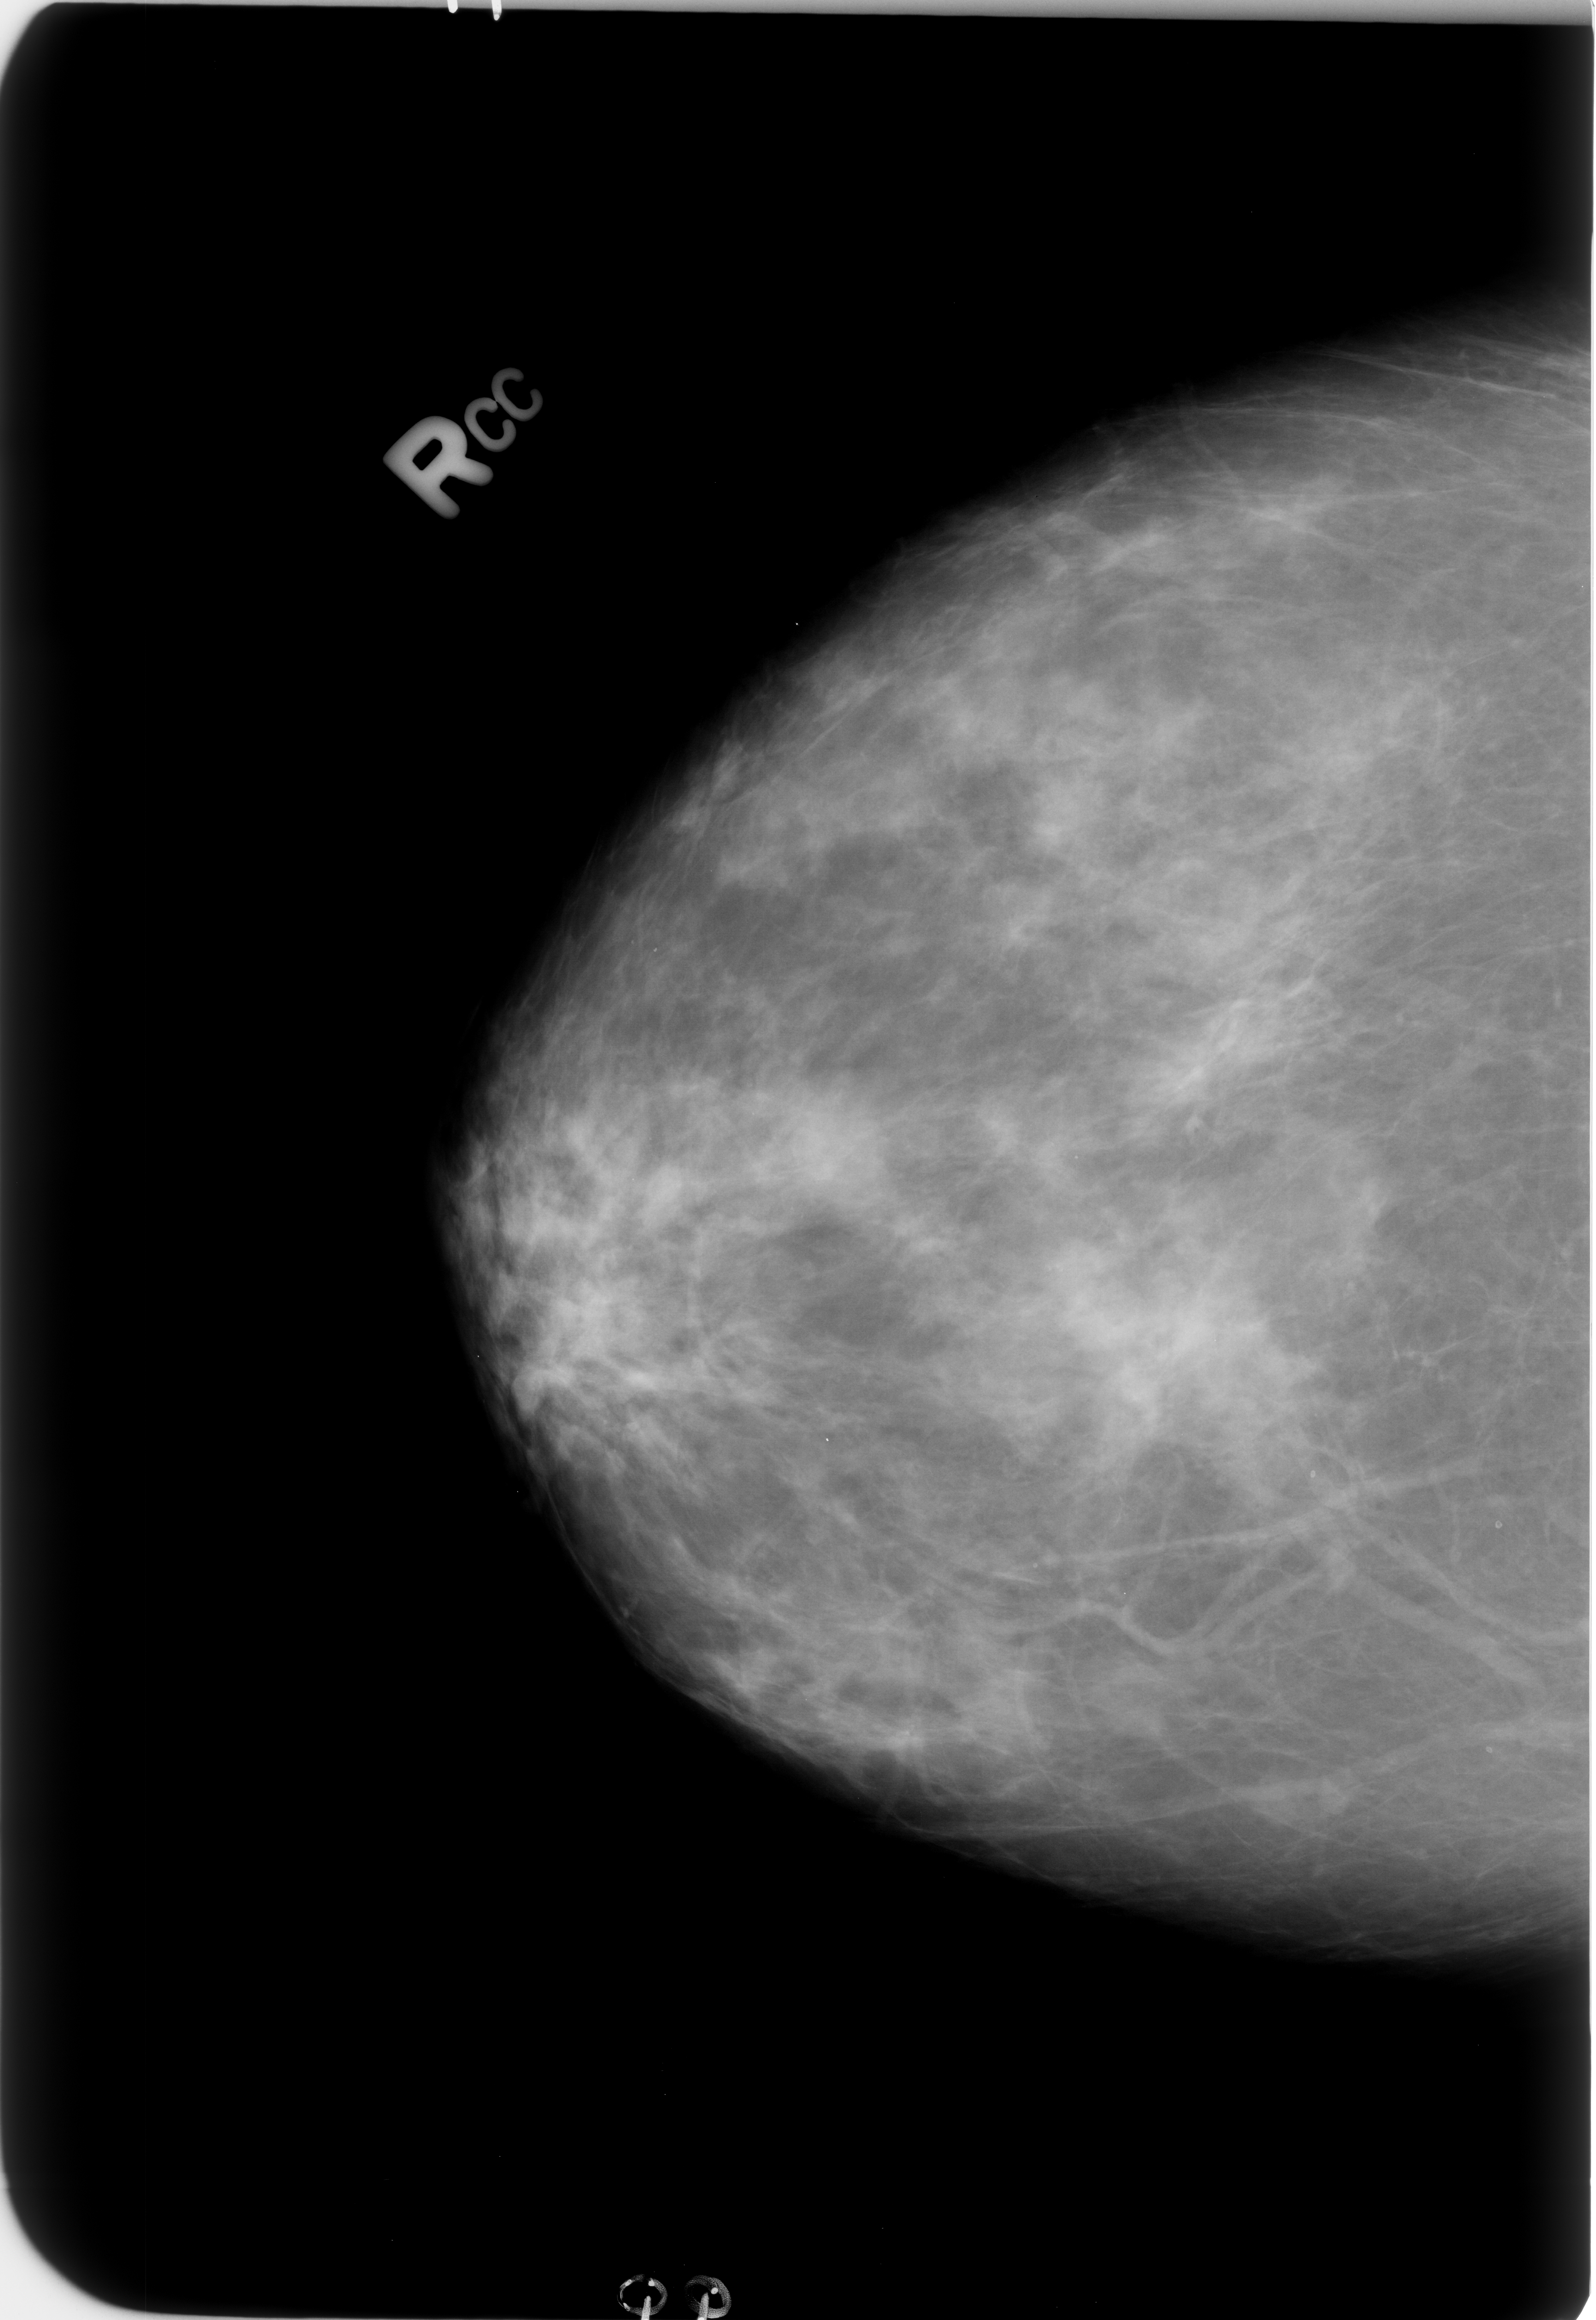
Scanned film-screen mammogram, right breast, CC view, breast composition: scattered fibroglandular densities (BI-RADS density category 2 of 4).
Abnormality record for this image: Finding 1 of 3: calcifications, morphology lucent center; BI-RADS assessment category 2; subtlety rating 3 on a 1 (subtle) to 5 (obvious) scale; benign; no additional work-up was recommended (benign without callback). Finding 2 of 3: calcifications, morphology lucent center; BI-RADS assessment category 2; subtlety rating 3 on a 1 (subtle) to 5 (obvious) scale; benign without callback (not worked up further). Finding 3 of 3: calcifications, morphology lucent center; BI-RADS assessment category 2; subtlety rating 3 on a 1 (subtle) to 5 (obvious) scale; benign without callback (not worked up further).